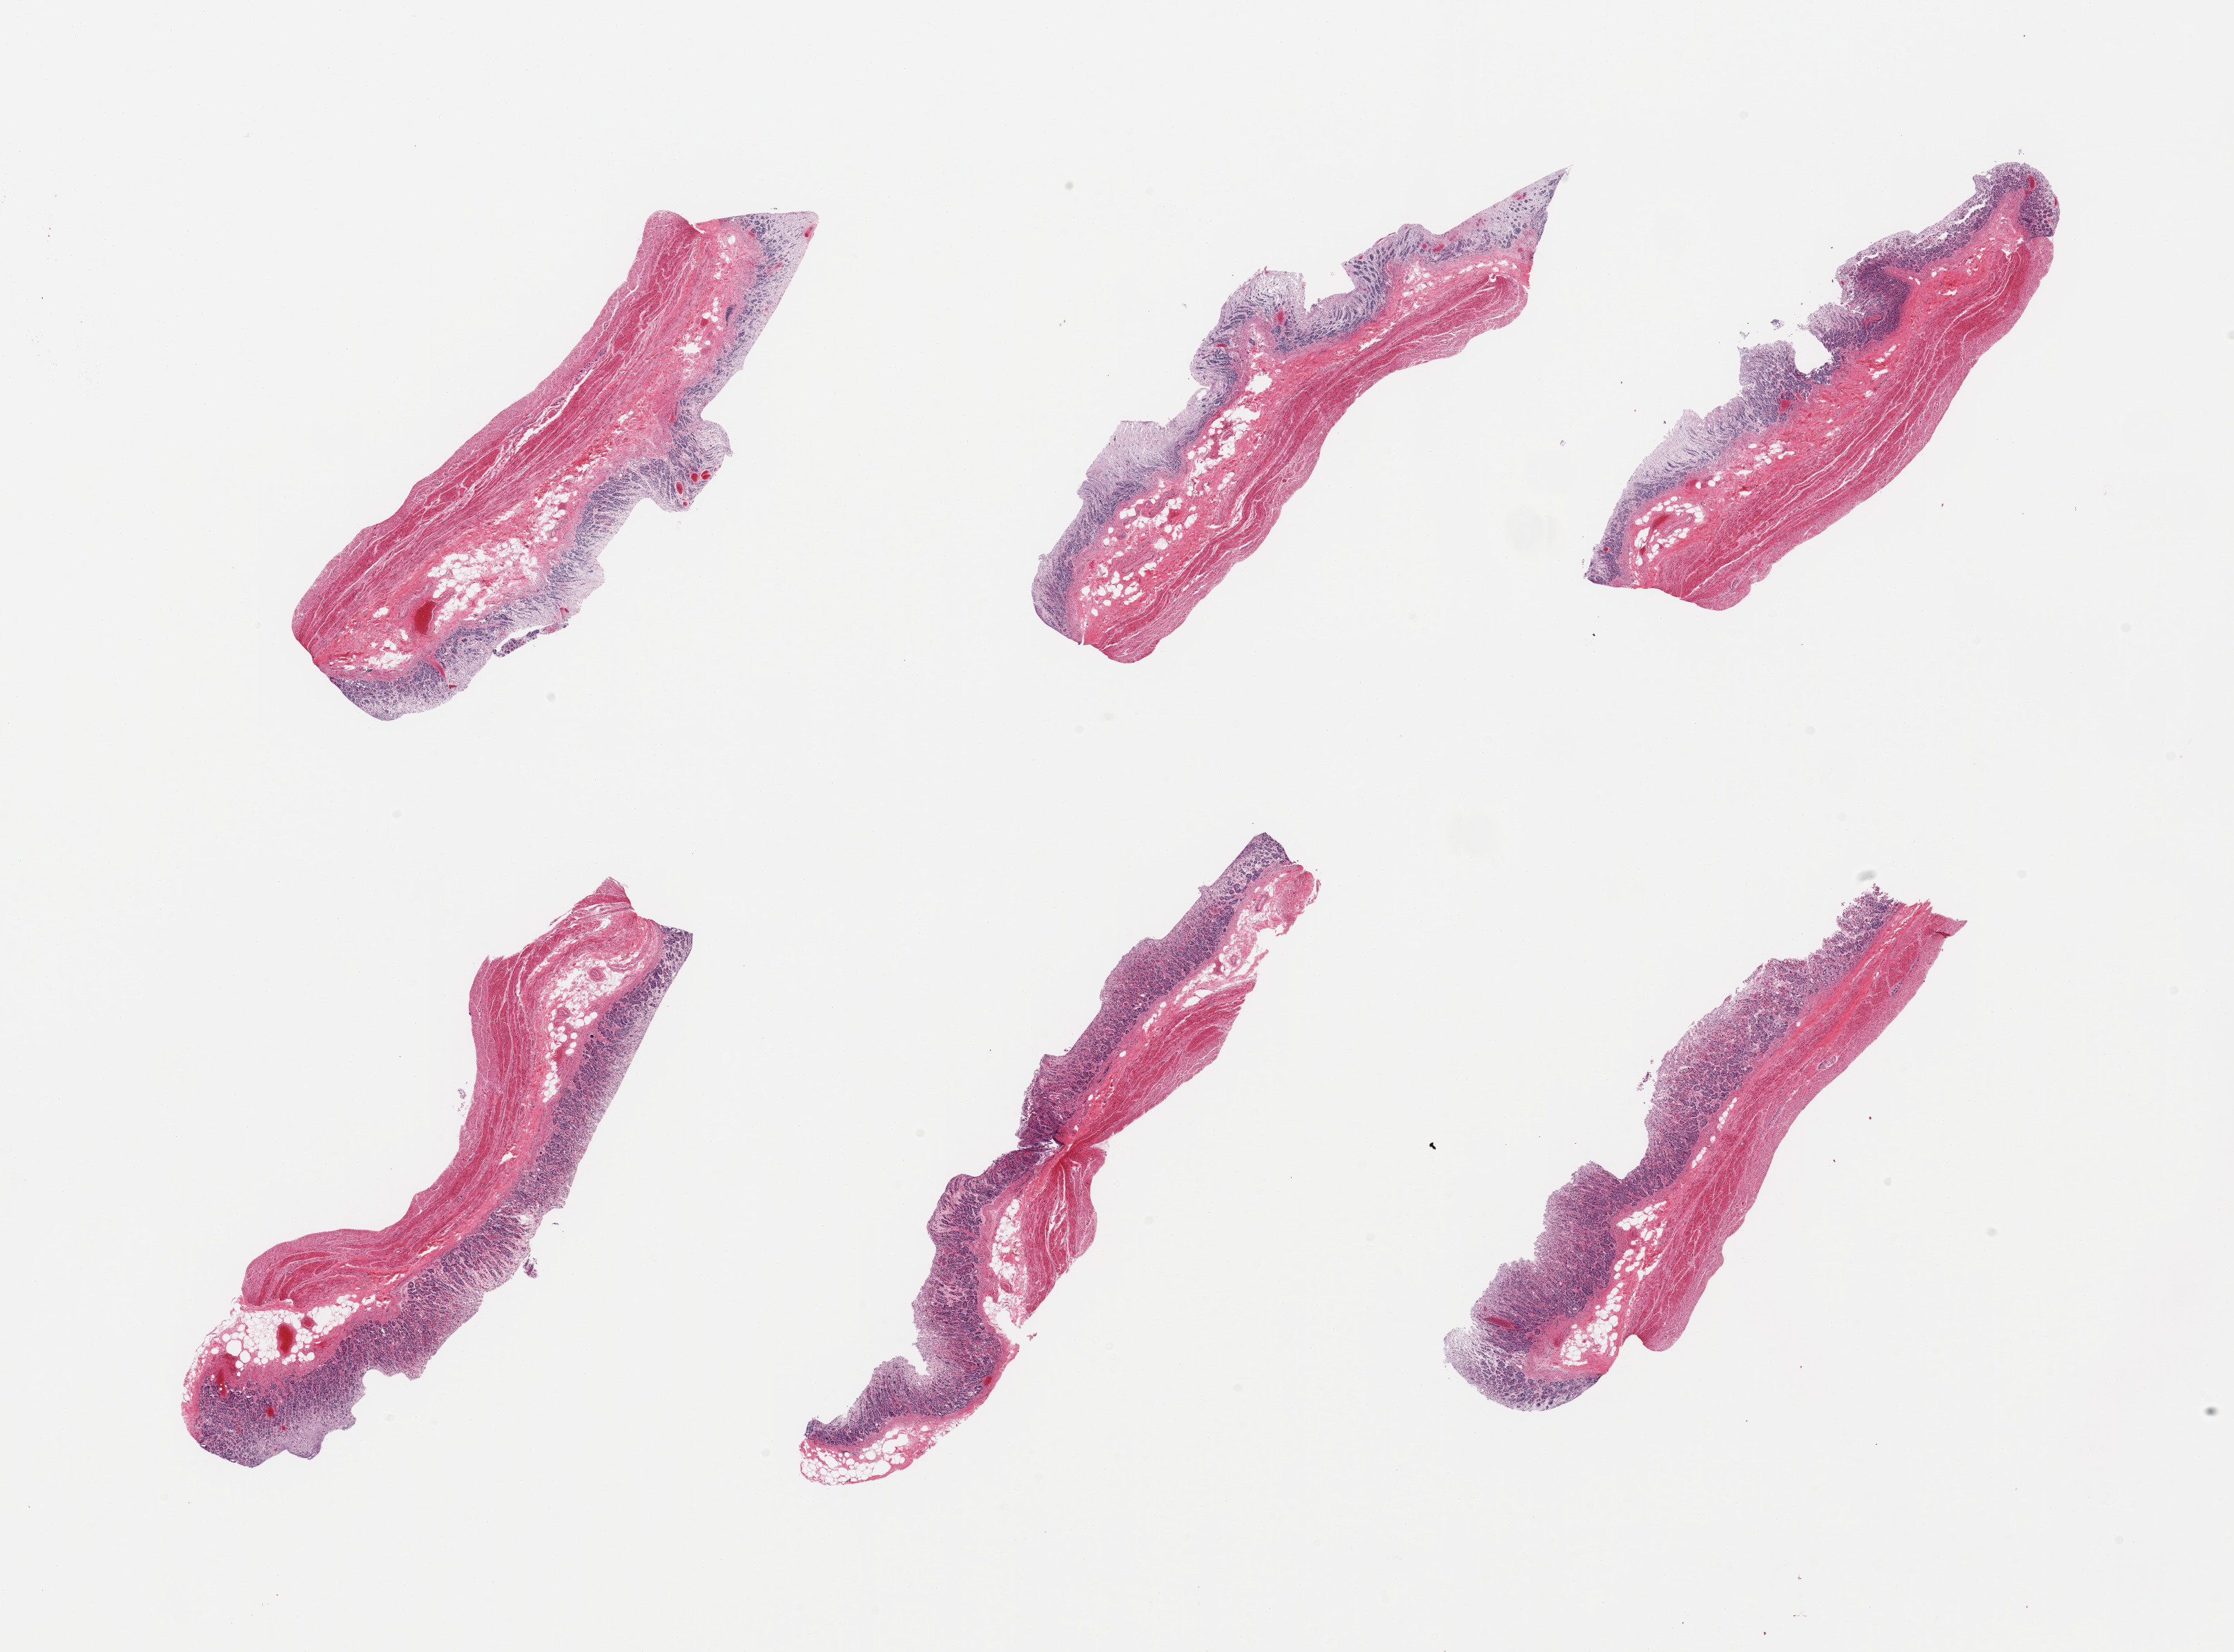
Digitized haematoxylin and eosin-stained section — a low-resolution overview of the entire scanned area, about 25.6 x 18.9 mm. PAXgene-fixed paraffin-embedded (PFPE) section. Sampled site (target tissue): stomach. Donor tissue sample. Donor sex: female.
* pathologist's review note for this sample: 6 pieces; mucosa largely autolyzed; muscularis intact